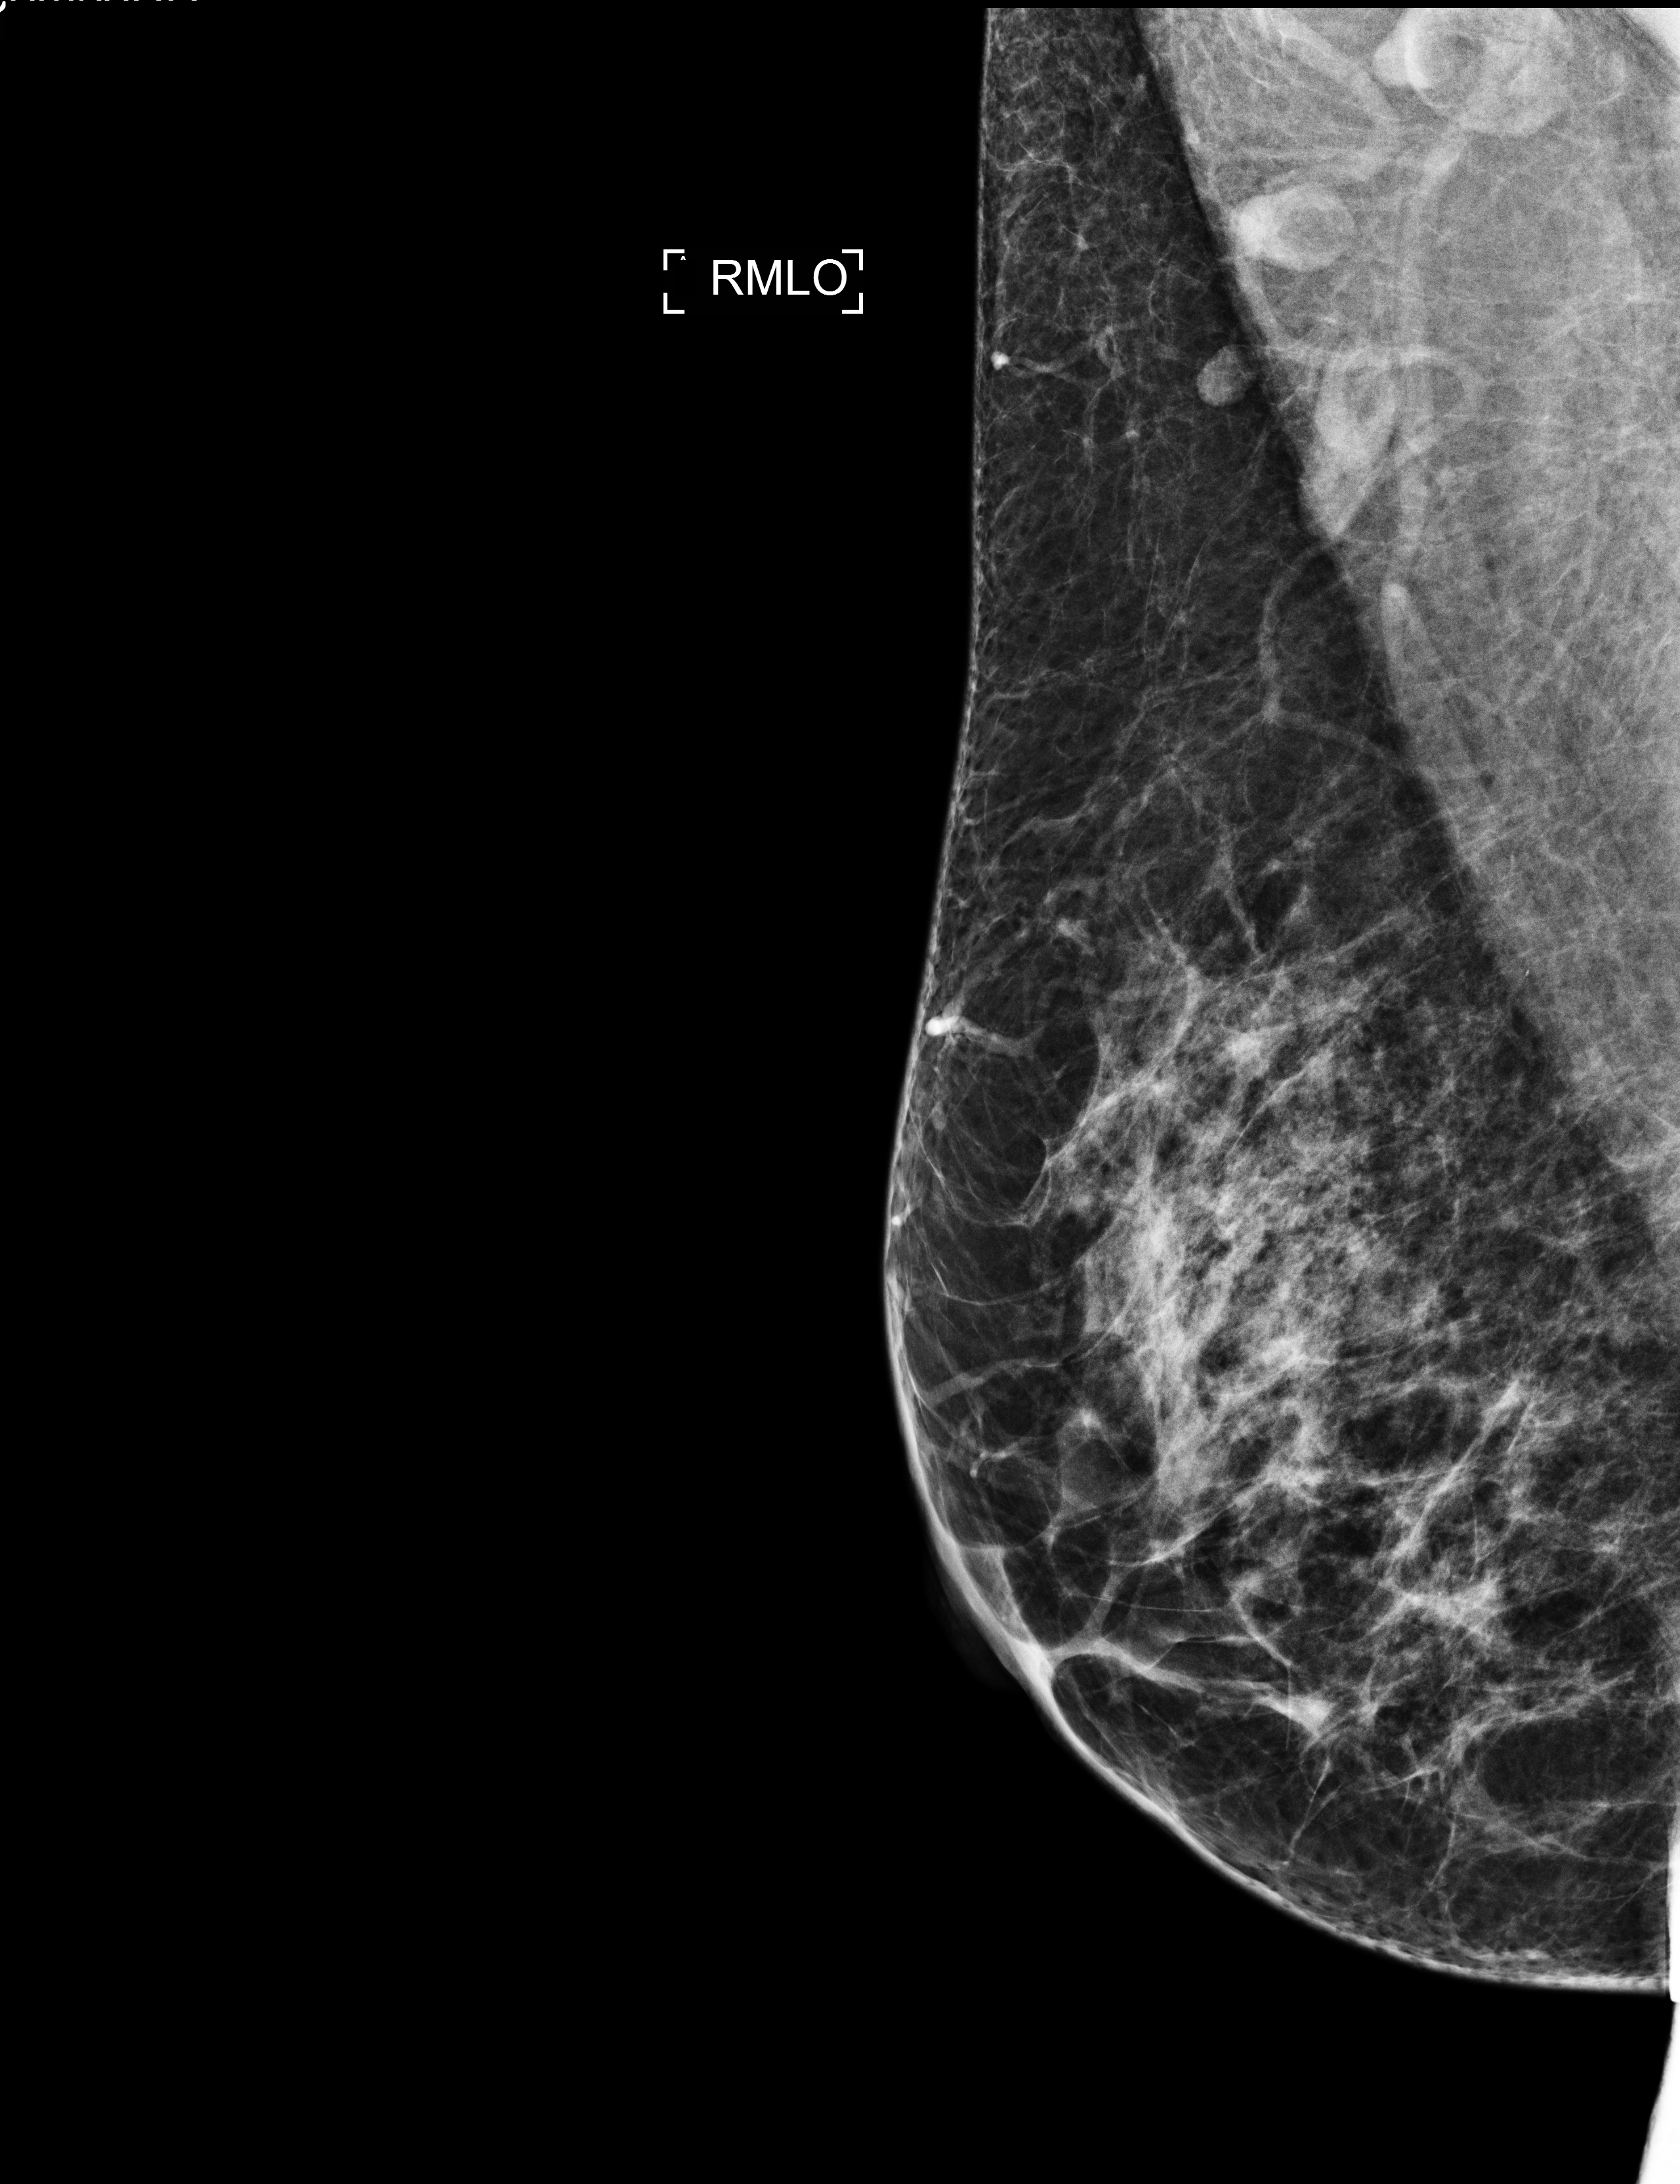
Digital mammogram (FFDM); right breast; mediolateral oblique (MLO) view; annual screening mammography examination. Patient aged 44 years (female).
BI-RADS breast density category at the screening exam (both breasts, scale 1–4): 3. Final BI-RADS category for the screening round (tomosynthesis exam, both breasts): category 1. Recall: no recall after this screen.